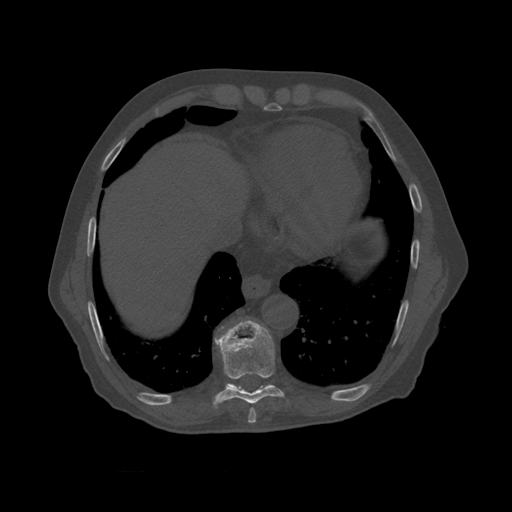
CT including the spine, one axial slice. Slice 443 of 450 in the series (ordered by position). Reconstruction kernel STANDARD. 120 kVp. Bone window (W 1800 / L 400 HU). 1.25 mm slice thickness. 512 × 512 image matrix. Patient age 75 years. From the clinical record (not read from this slice): primary cancer: prostate.
Annotated regions visible in this slice (semi-automatic segmentation, software-assisted and operator-edited):
- T8 vertebra: bounding box (x1, y1, x2, y2) in pixels: (215, 321, 285, 410)
- T9 vertebra: (226, 384, 242, 388)